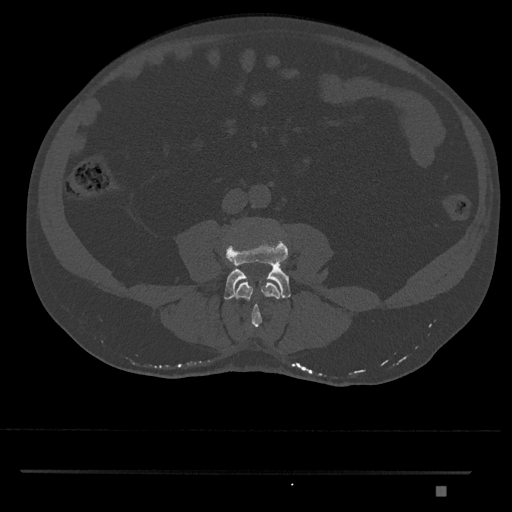
CT including the spine, one axial slice. Position 643 of 1134 along the scan axis. Reconstruction kernel Br40s/3. 120 kVp. Bone window (W 1800 / L 400 HU). 0.5 mm slice thickness. 512 × 512 image matrix, field of view 429 × 429 mm. Male patient, age 65 years. From the clinical record (not read from this slice): primary cancer: prostate.
Annotated regions visible in this slice (semi-automatically segmented with operator editing):
- L3 vertebra: bounding box [x1, y1, x2, y2] px = [236, 282, 280, 328]
- L4 vertebra: [224, 228, 291, 300]